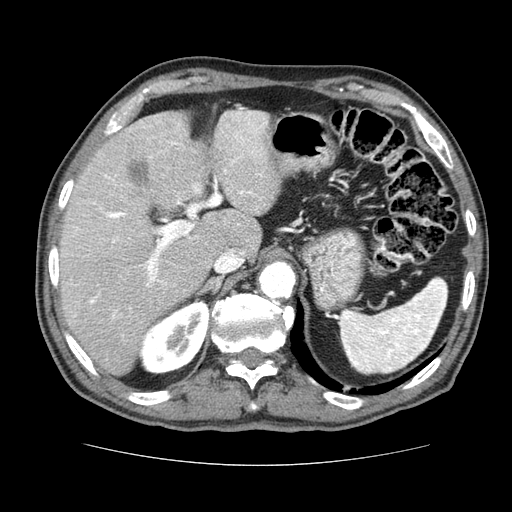
Contrast-enhanced abdominal CT (liver protocol), one axial slice; slice 49 of 79 in the series (ordered by position); reconstruction kernel STANDARD; soft-tissue window (W 400 / L 40 HU); 512 × 512 image matrix. From the clinical record (not read from this slice): diagnosis: hepatocellular carcinoma (patient treated with transarterial chemoembolisation; whether this scan precedes or follows treatment is not stated here); TNM stage (as recorded): Stage-I; Child-Pugh class: A; tumour nodularity: uninodular.
Structures marked on this image (semi-automatic segmentation, software-assisted and operator-edited):
- liver parenchyma outside the tumour (the mass and vessels are separate outlines, so this box may not span the whole liver): bounding box (x1, y1, x2, y2) in pixels: (58, 108, 280, 374)
- liver vessels: (74, 111, 267, 318)